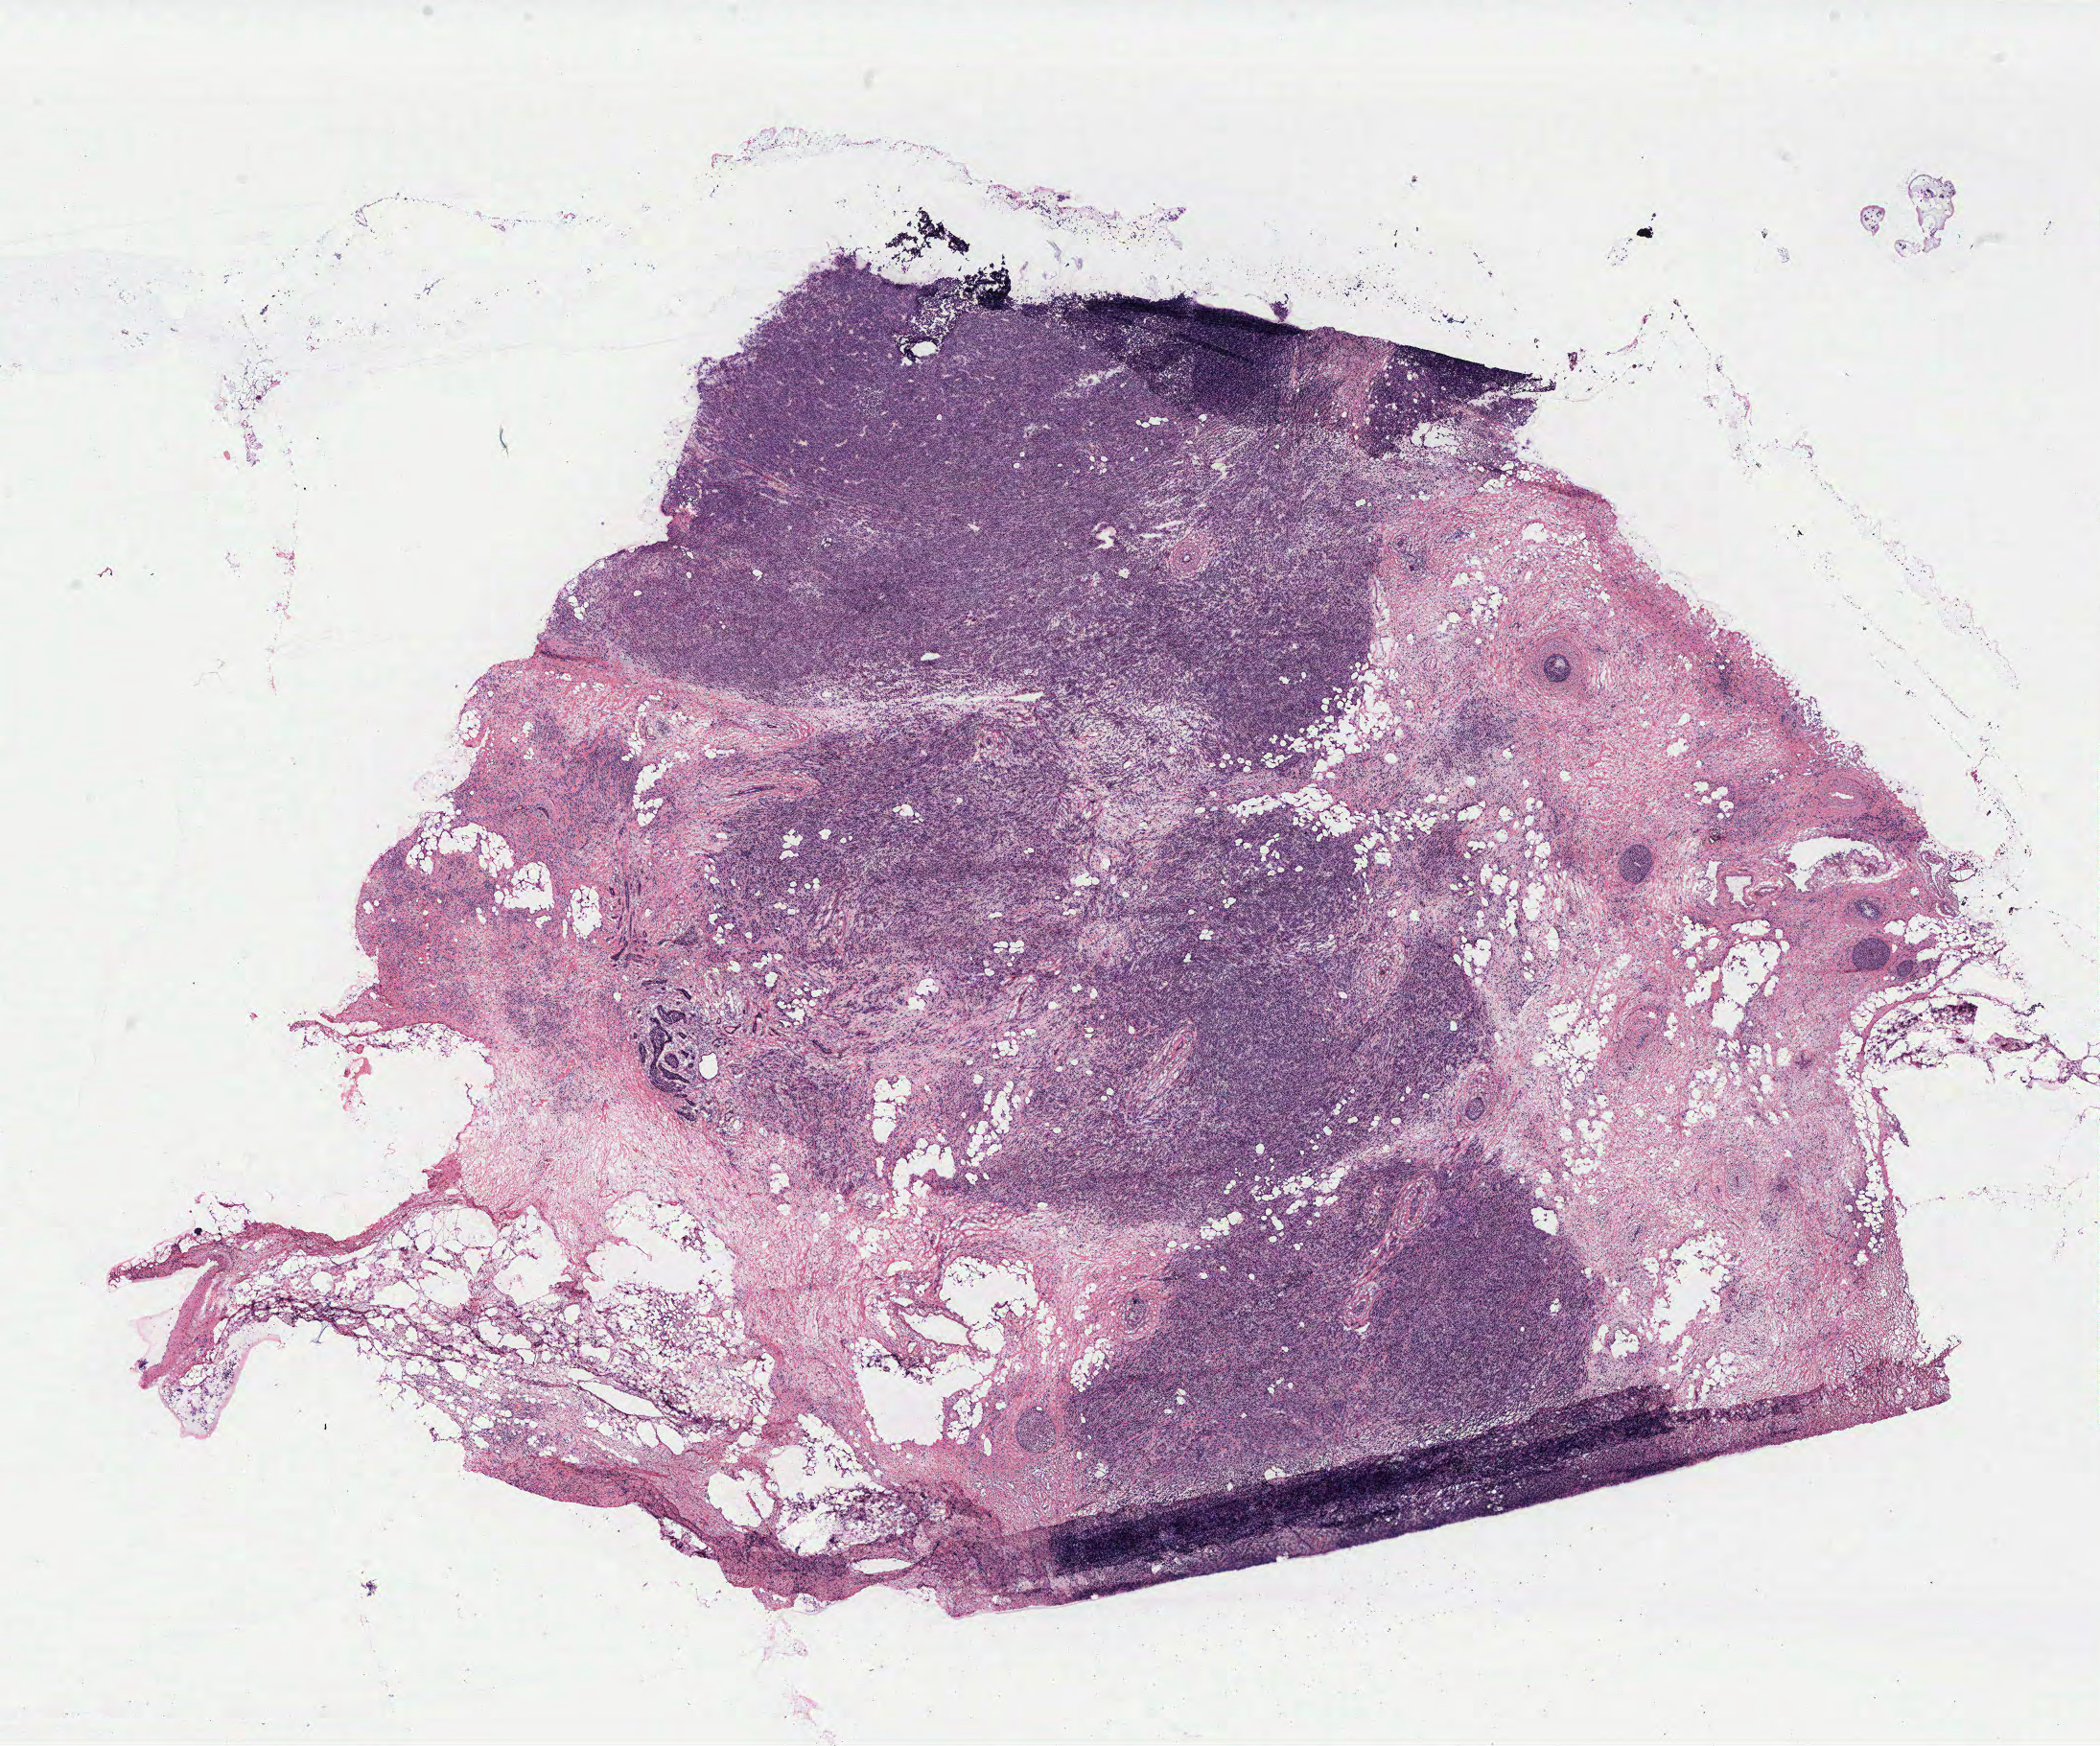
Whole-slide histology image, H&E-stained, whole scanned area (about 17.5 x 14.6 mm, slide scanned at 40x) shown as a low-resolution overview; breast, tissue type not recorded. 69-year-old female patient.
• patient diagnosis: Infiltrating lobular carcinoma, NOS